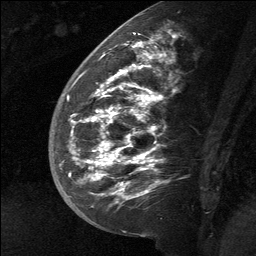
Breast MRI (dynamic contrast-enhanced), one sagittal slice; position 26 of 64 along the scan axis; dynamic contrast-enhanced study with each time point stored as its own series, time point 2 of 3 at this slice position (early post-contrast, ordered by acquisition time); 1.5 T; TE 4.8 ms, TR 27 ms; 2 mm slice thickness; 256 × 256 image matrix, field of view 180 × 180 mm. Patient: female, 39 years. Case-level facts recorded for this patient, not image findings: setting: breast cancer imaged before/during neoadjuvant chemotherapy; receptor status: HER2-positive.
Annotated regions visible in this slice (semi-automatic segmentation, software-assisted and operator-edited):
- analysis volume of interest (the breast-tissue region the enhancement analysis was run in; not a lesion): bounding box <58,40,168,217> (left, top, right, bottom; pixels)
- tumour enhancement mask (voxels above the 90 % enhancement threshold inside the analysis volume of interest): <69,40,162,199>